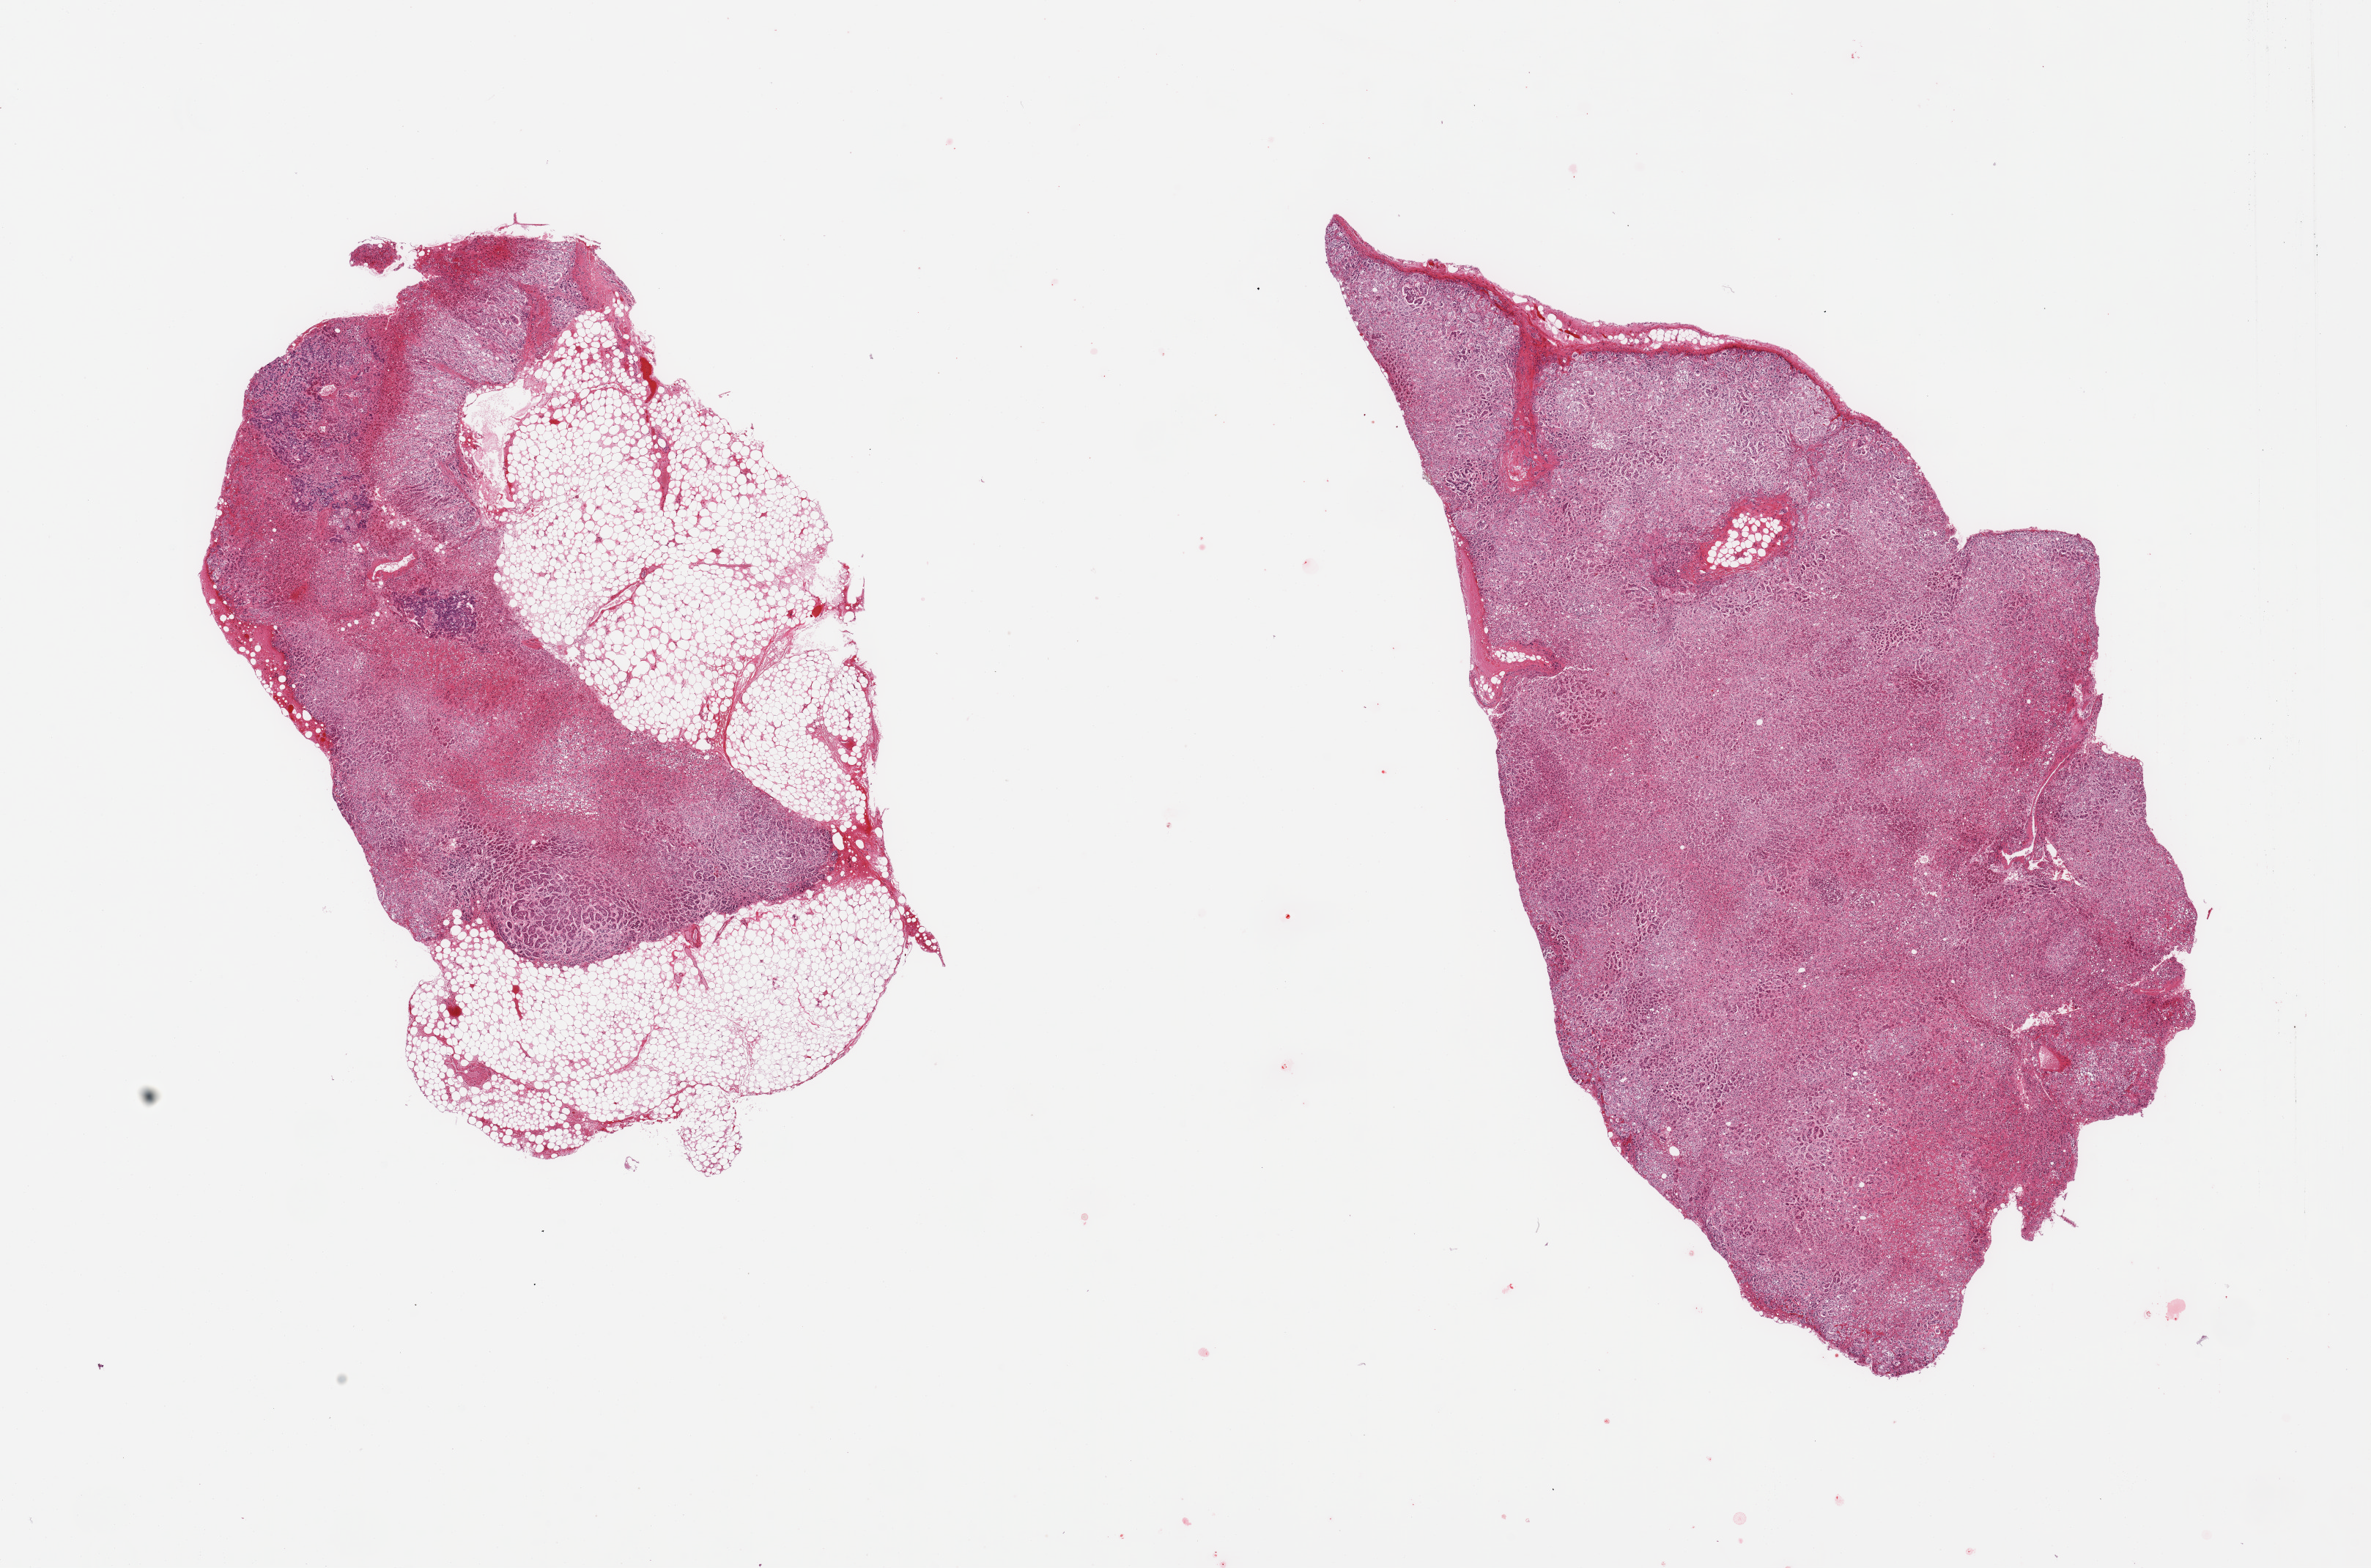
Hematoxylin and eosin (H&E) whole-slide image, a low-resolution overview of the entire scanned area, about 25.6 x 16.9 mm; PAXgene-fixed, paraffin-embedded tissue; sampled site (target tissue): adrenal gland; tissue donor sample. Donor sex: female.
Reviewer comment on this tissue sample: 2 pieces; cortex and medulla, one is ~40% fat.